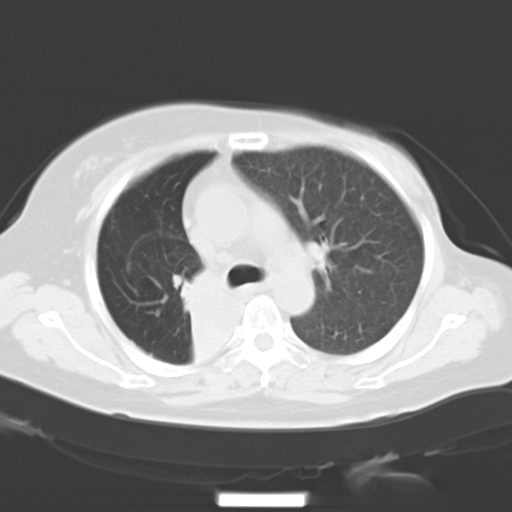
Chest CT, one axial slice. Position 21 of 30 along the scan axis. Reconstruction kernel B40f. 120 kVp. Lung window (W 1500 / L -600 HU). 8 mm slice thickness. 512 × 512 image matrix, field of view 331 × 331 mm. Patient: female, 53 years. Case-level facts recorded for this patient, not image findings: clinical TNM (as recorded): T2b N1 M0.
Outlined on this slice (rectangle marked by the reading radiologist):
- lung tumour (recorded histology: adenocarcinoma): box from (x=167, y=269) to (x=234, y=356) px